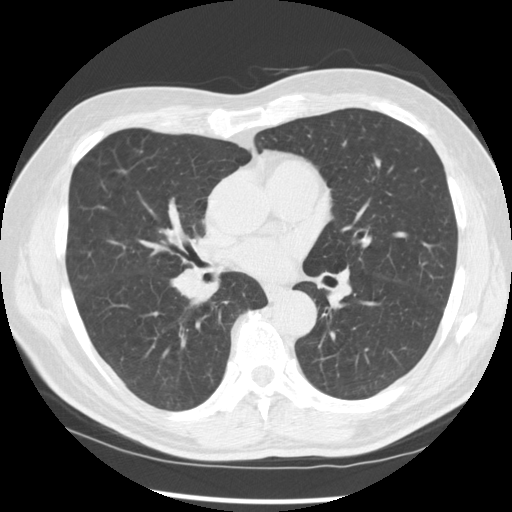
Low-dose screening chest CT, one axial slice. Reconstruction kernel STANDARD. 120 kVp. Lung window (W 1500 / L -600 HU). 2.5 mm slice thickness. 512 × 512 image matrix, field of view 365 × 365 mm.
Structures marked on this image (outlined manually by an expert reader):
- lesion 1 (tumor, middle lobe of right lung): bounding box [x1, y1, x2, y2] px = [170, 268, 210, 302]